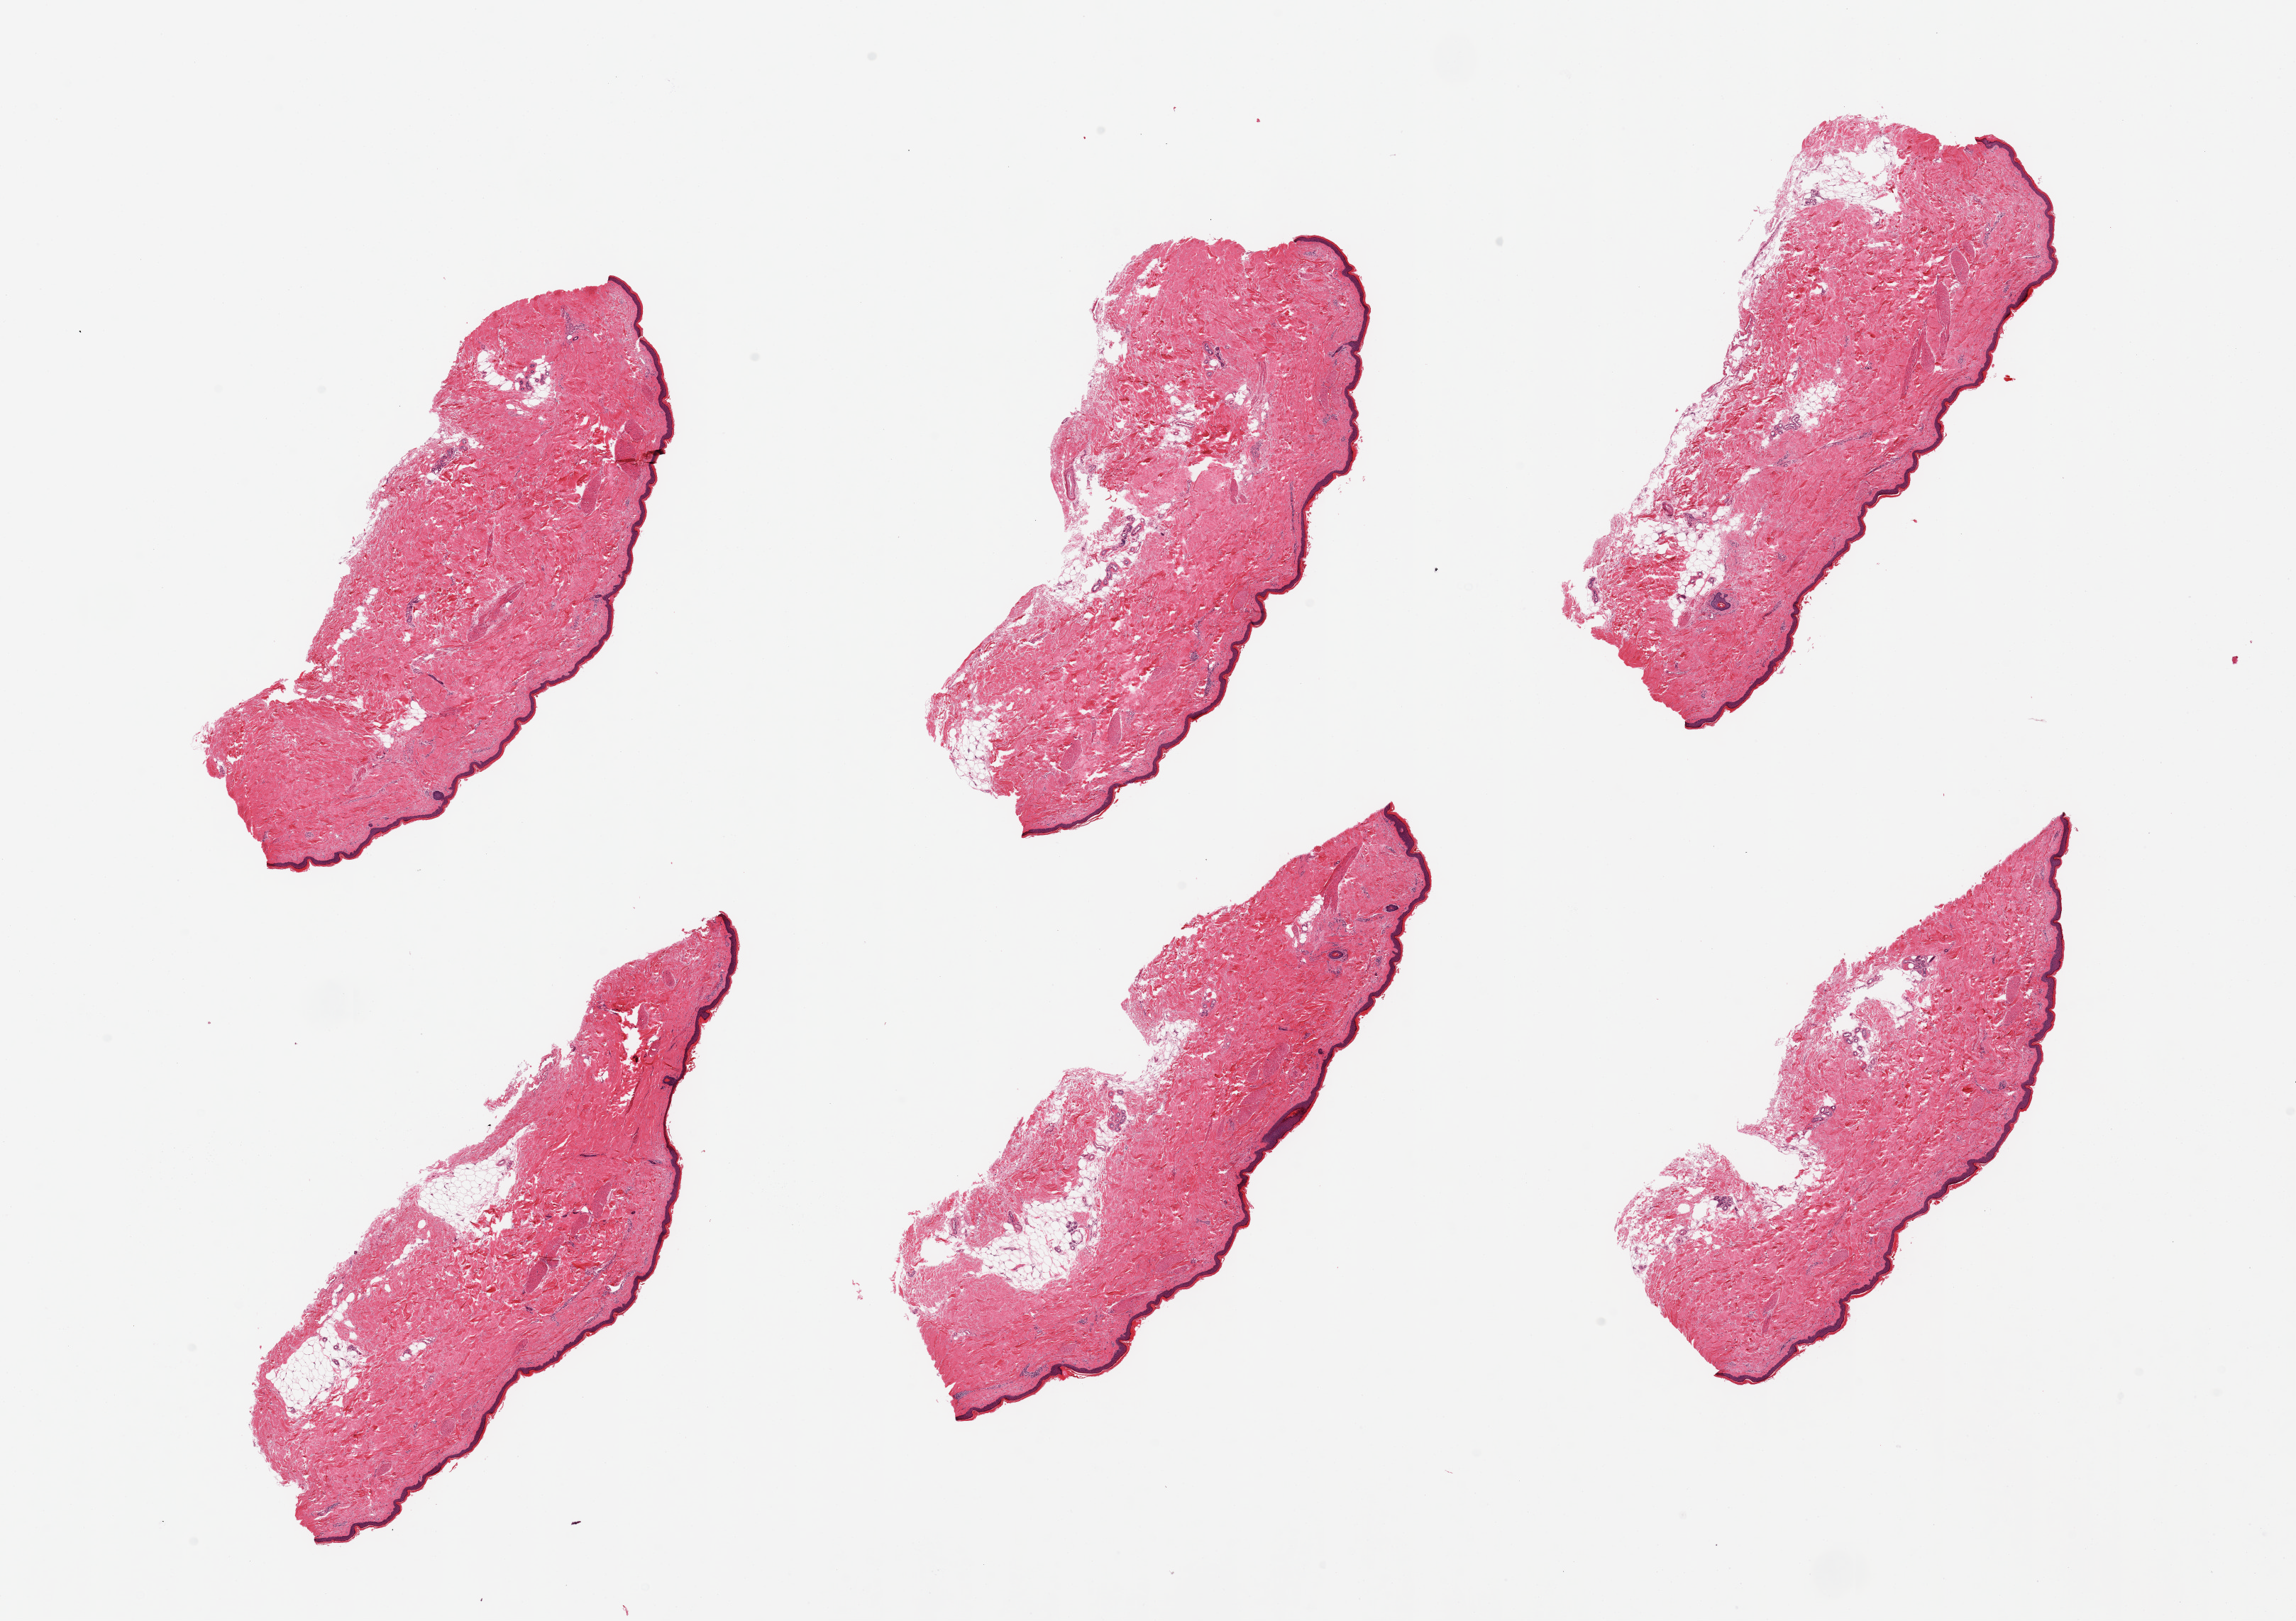
H&E whole-slide image, a low-resolution overview of the entire scanned area, about 25.6 x 18.1 mm (from a 20x scan). PAXgene-fixed paraffin-embedded (PFPE) section. Section of skin of lower leg (target tissue). Donor tissue sample.
- review note (as recorded): 6 pieces, trace dermal fat; squamous epithelium is ~50 microns